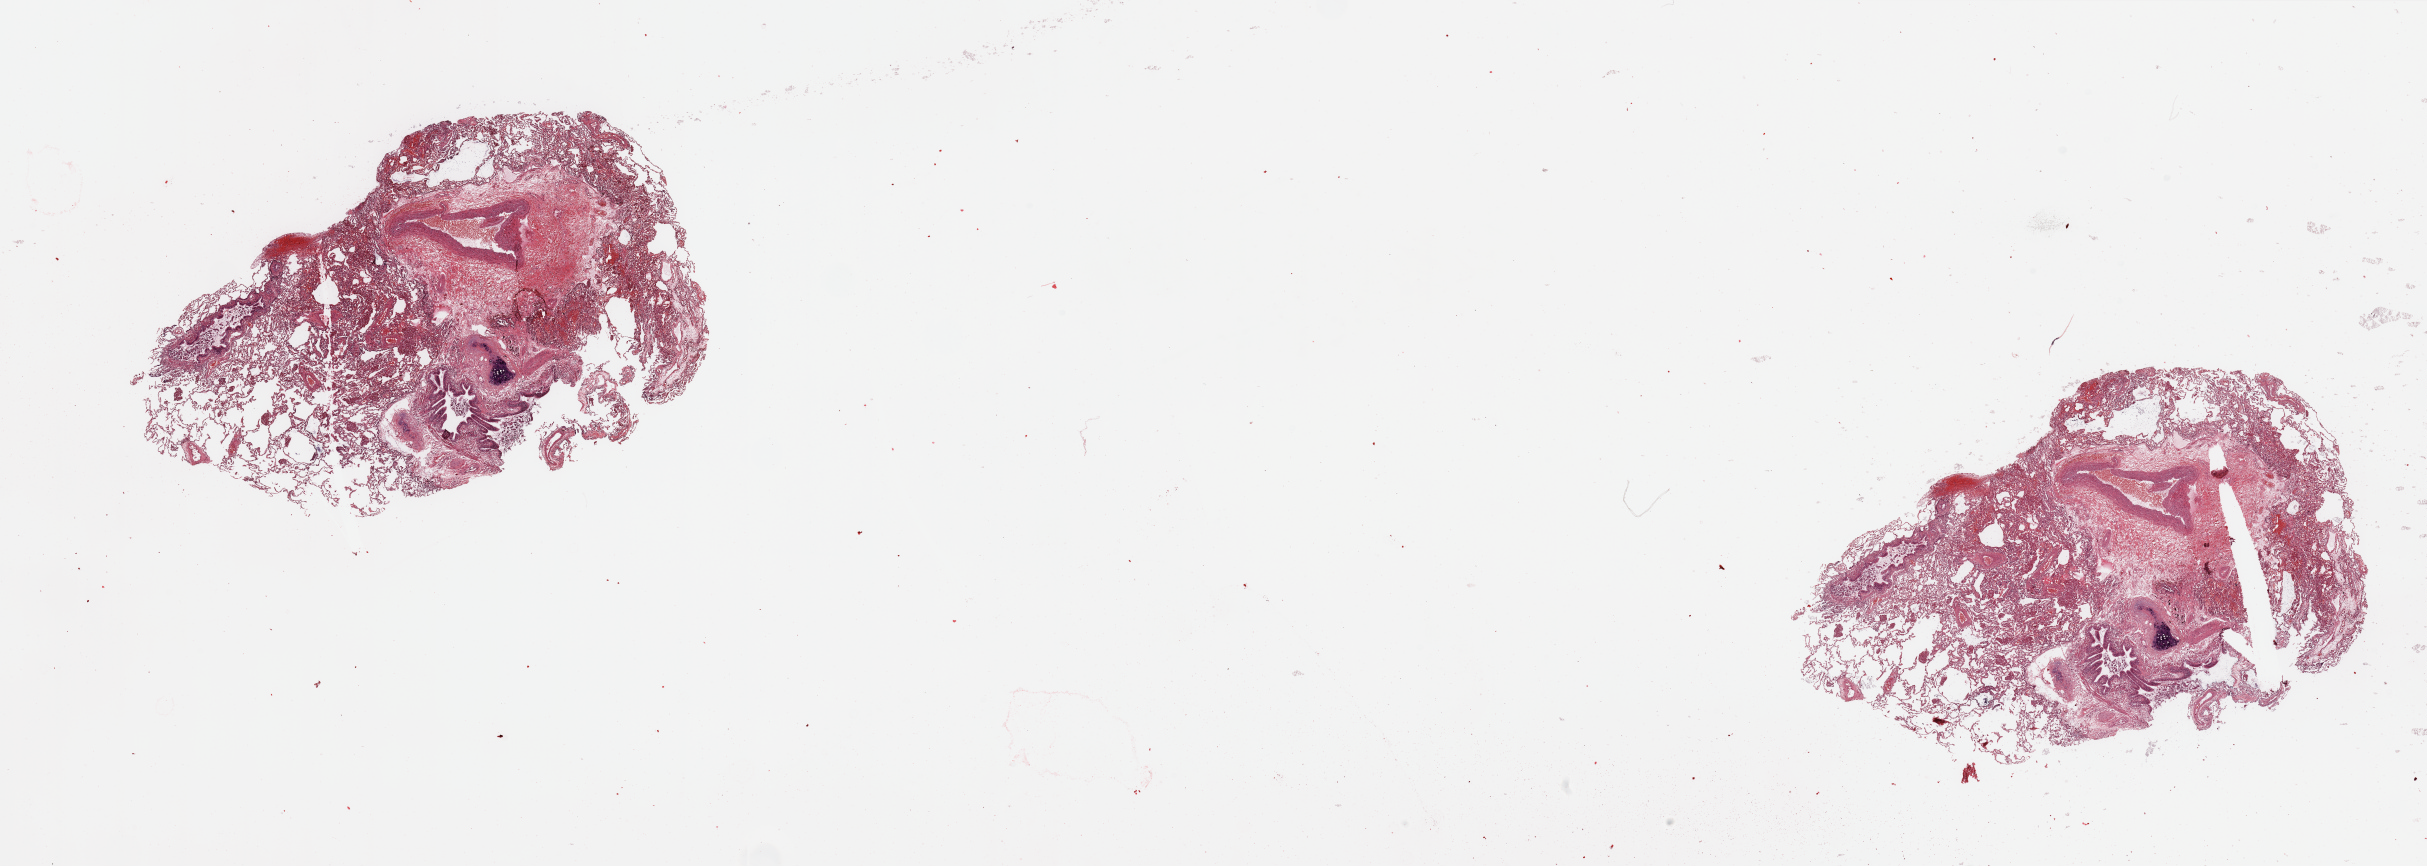
H&E-stained whole-slide image — whole scanned area (about 38.4 x 13.7 mm, from a 20x scan) shown as a low-resolution overview; normal (non-tumour) tissue sample, lung. 59-year-old male patient.
This section: normal (non-tumour) tissue from the same patient. Patient diagnosis: Adenocarcinoma, NOS.